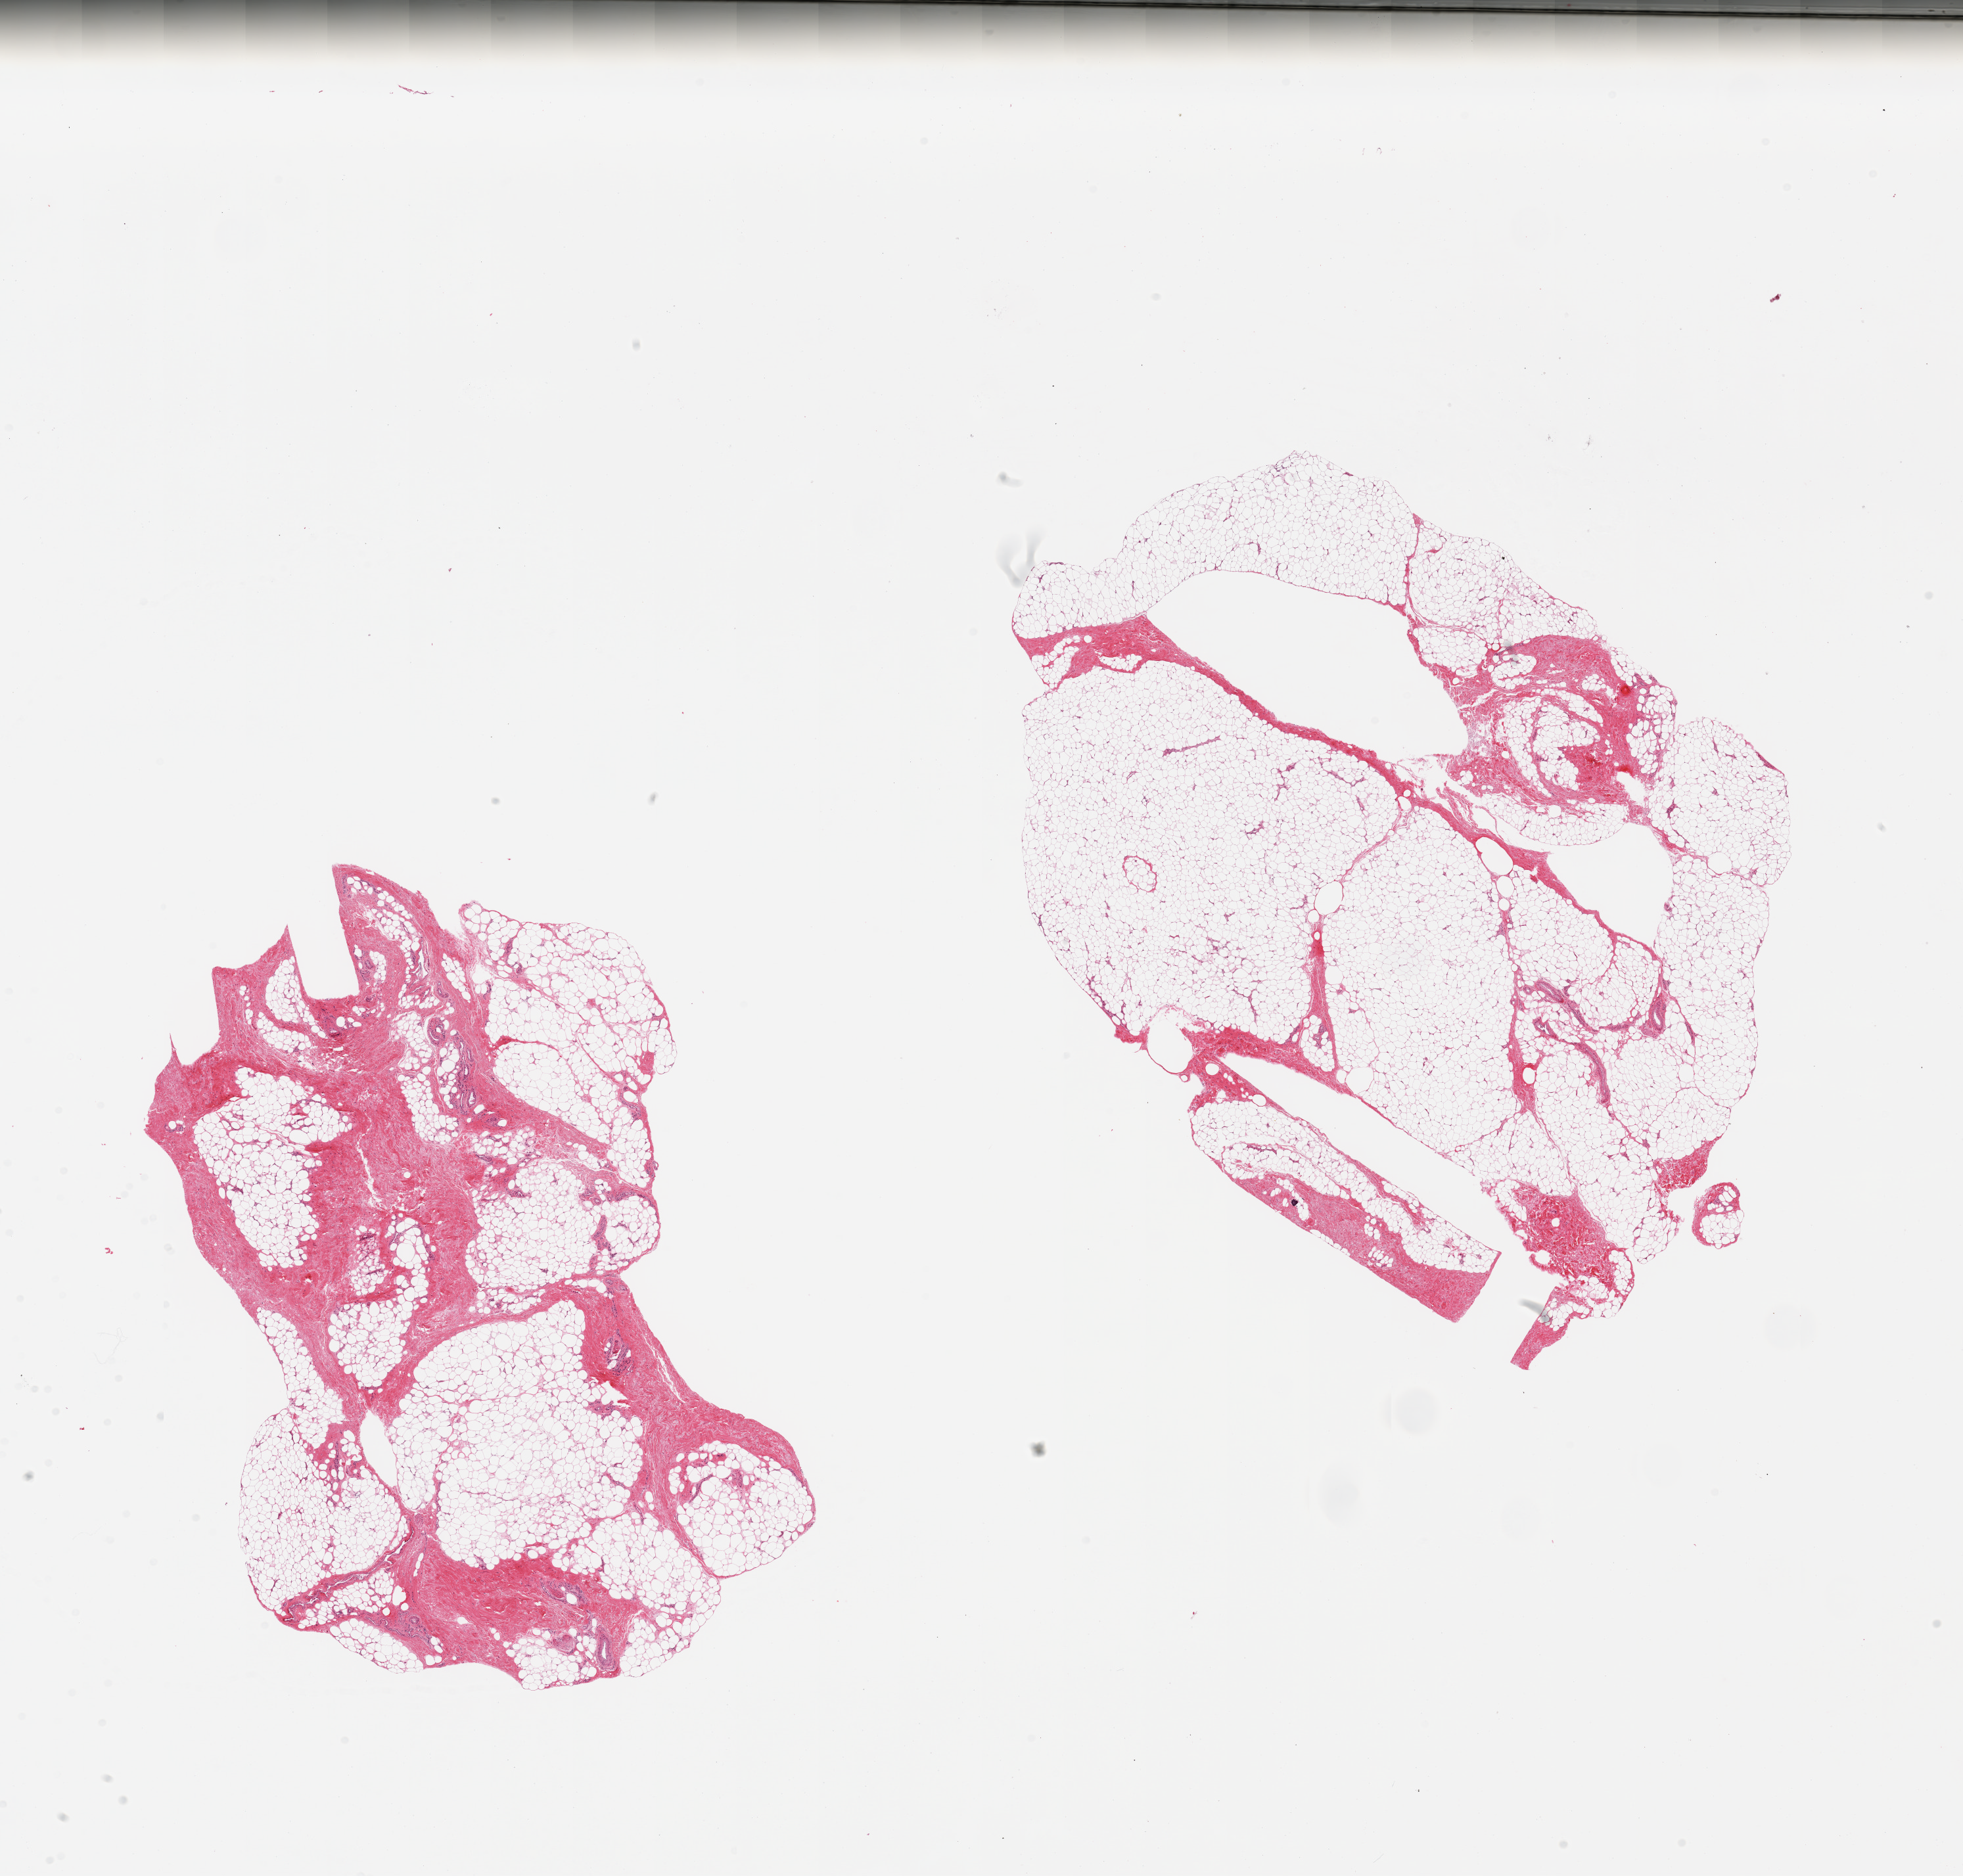
Haematoxylin and eosin whole-slide image, shown as a low-resolution overview of the whole scanned area (about 23.6 x 22.6 mm, acquisition: 20x scan), PAXgene-fixed, paraffin-embedded tissue, sampled site (target tissue): adipose tissue, donor tissue sample. Donor sex: male.
Review note (as recorded): 2 pieces, ~40% fibrous/fascial tissue.